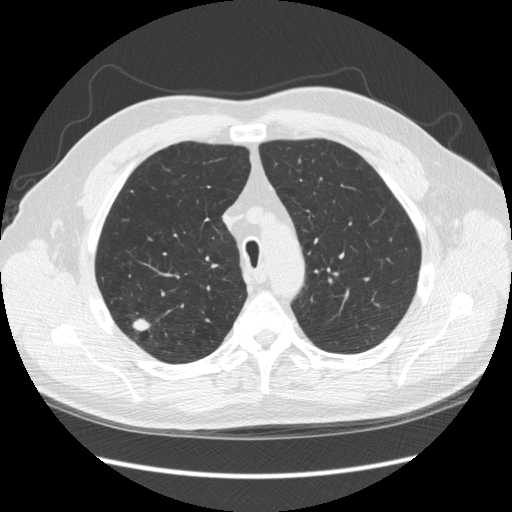
Low-dose screening chest CT, axial slice; third screening round (two years after baseline); lung window (W 1500 / L -600 HU); standard (soft-tissue) reconstruction kernel (STANDARD); 120 kVp. Male participant, aged 64 years at enrolment.
Expert reader's lesion annotation, bounding box [x1, y1, x2, y2] px = [118, 313, 168, 355]. The screening reader recorded 4 non-calcified nodules or masses ≥4 mm on this exam (right upper lobe, right upper lobe, right upper lobe, right upper lobe); which of them this box marks is not recorded. Official screen result: positive, other. Lung cancer was diagnosed 15 days after this screen: adenocarcinoma, NOS, right upper lobe, moderately differentiated (G2), stage IA (AJCC 6th edition), 14 mm at pathology.